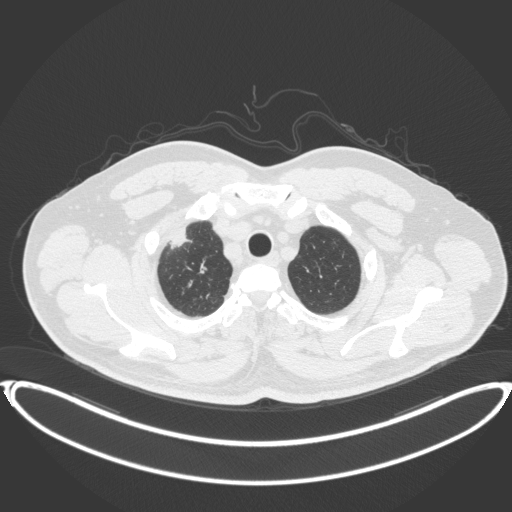
Chest CT, one axial slice; position 343 of 399 along the scan axis; reconstruction kernel B31f; lung window (W 1500 / L -600 HU); 1 mm slice thickness; 512 × 512 image matrix, field of view 445 × 445 mm. Patient: male, 53 years. Case-level facts recorded for this patient, not image findings: clinical TNM (as recorded): T2a N0 M0.
Structures marked on this image (bounding box drawn by a radiologist):
- lung tumour (recorded histology: adenocarcinoma): box from (x=164, y=215) to (x=201, y=258) px